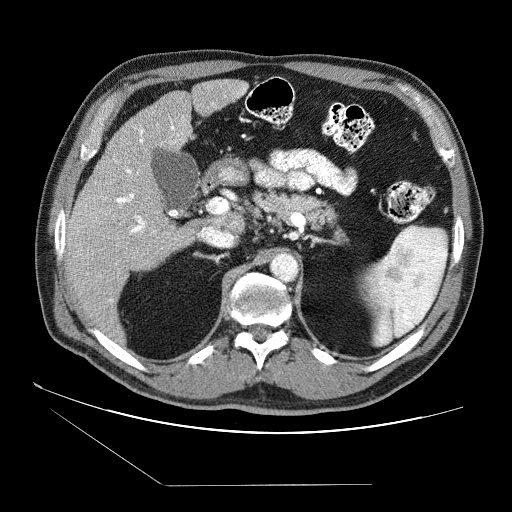
Contrast-enhanced abdominal CT (liver protocol), one axial slice; position 42 of 87 along the scan axis; 120 kVp; soft-tissue window (W 400 / L 40 HU); 2.5 mm slice thickness; 512 × 512 image matrix, field of view 400 × 400 mm. Case-level facts recorded for this patient, not image findings: diagnosis: hepatocellular carcinoma (patient treated with transarterial chemoembolisation; whether this scan precedes or follows treatment is not stated here); TNM stage (as recorded): Stage-II; Child-Pugh class: B; tumour differentiation: no biopsy; tumour nodularity: multinodular.
Structures marked on this image (semi-automatically segmented with operator editing):
- liver parenchyma outside the tumour (the mass and vessels are separate outlines, so this box may not span the whole liver): bounding box [x1, y1, x2, y2] px = [64, 78, 248, 332]
- liver vessels: [72, 87, 246, 302]